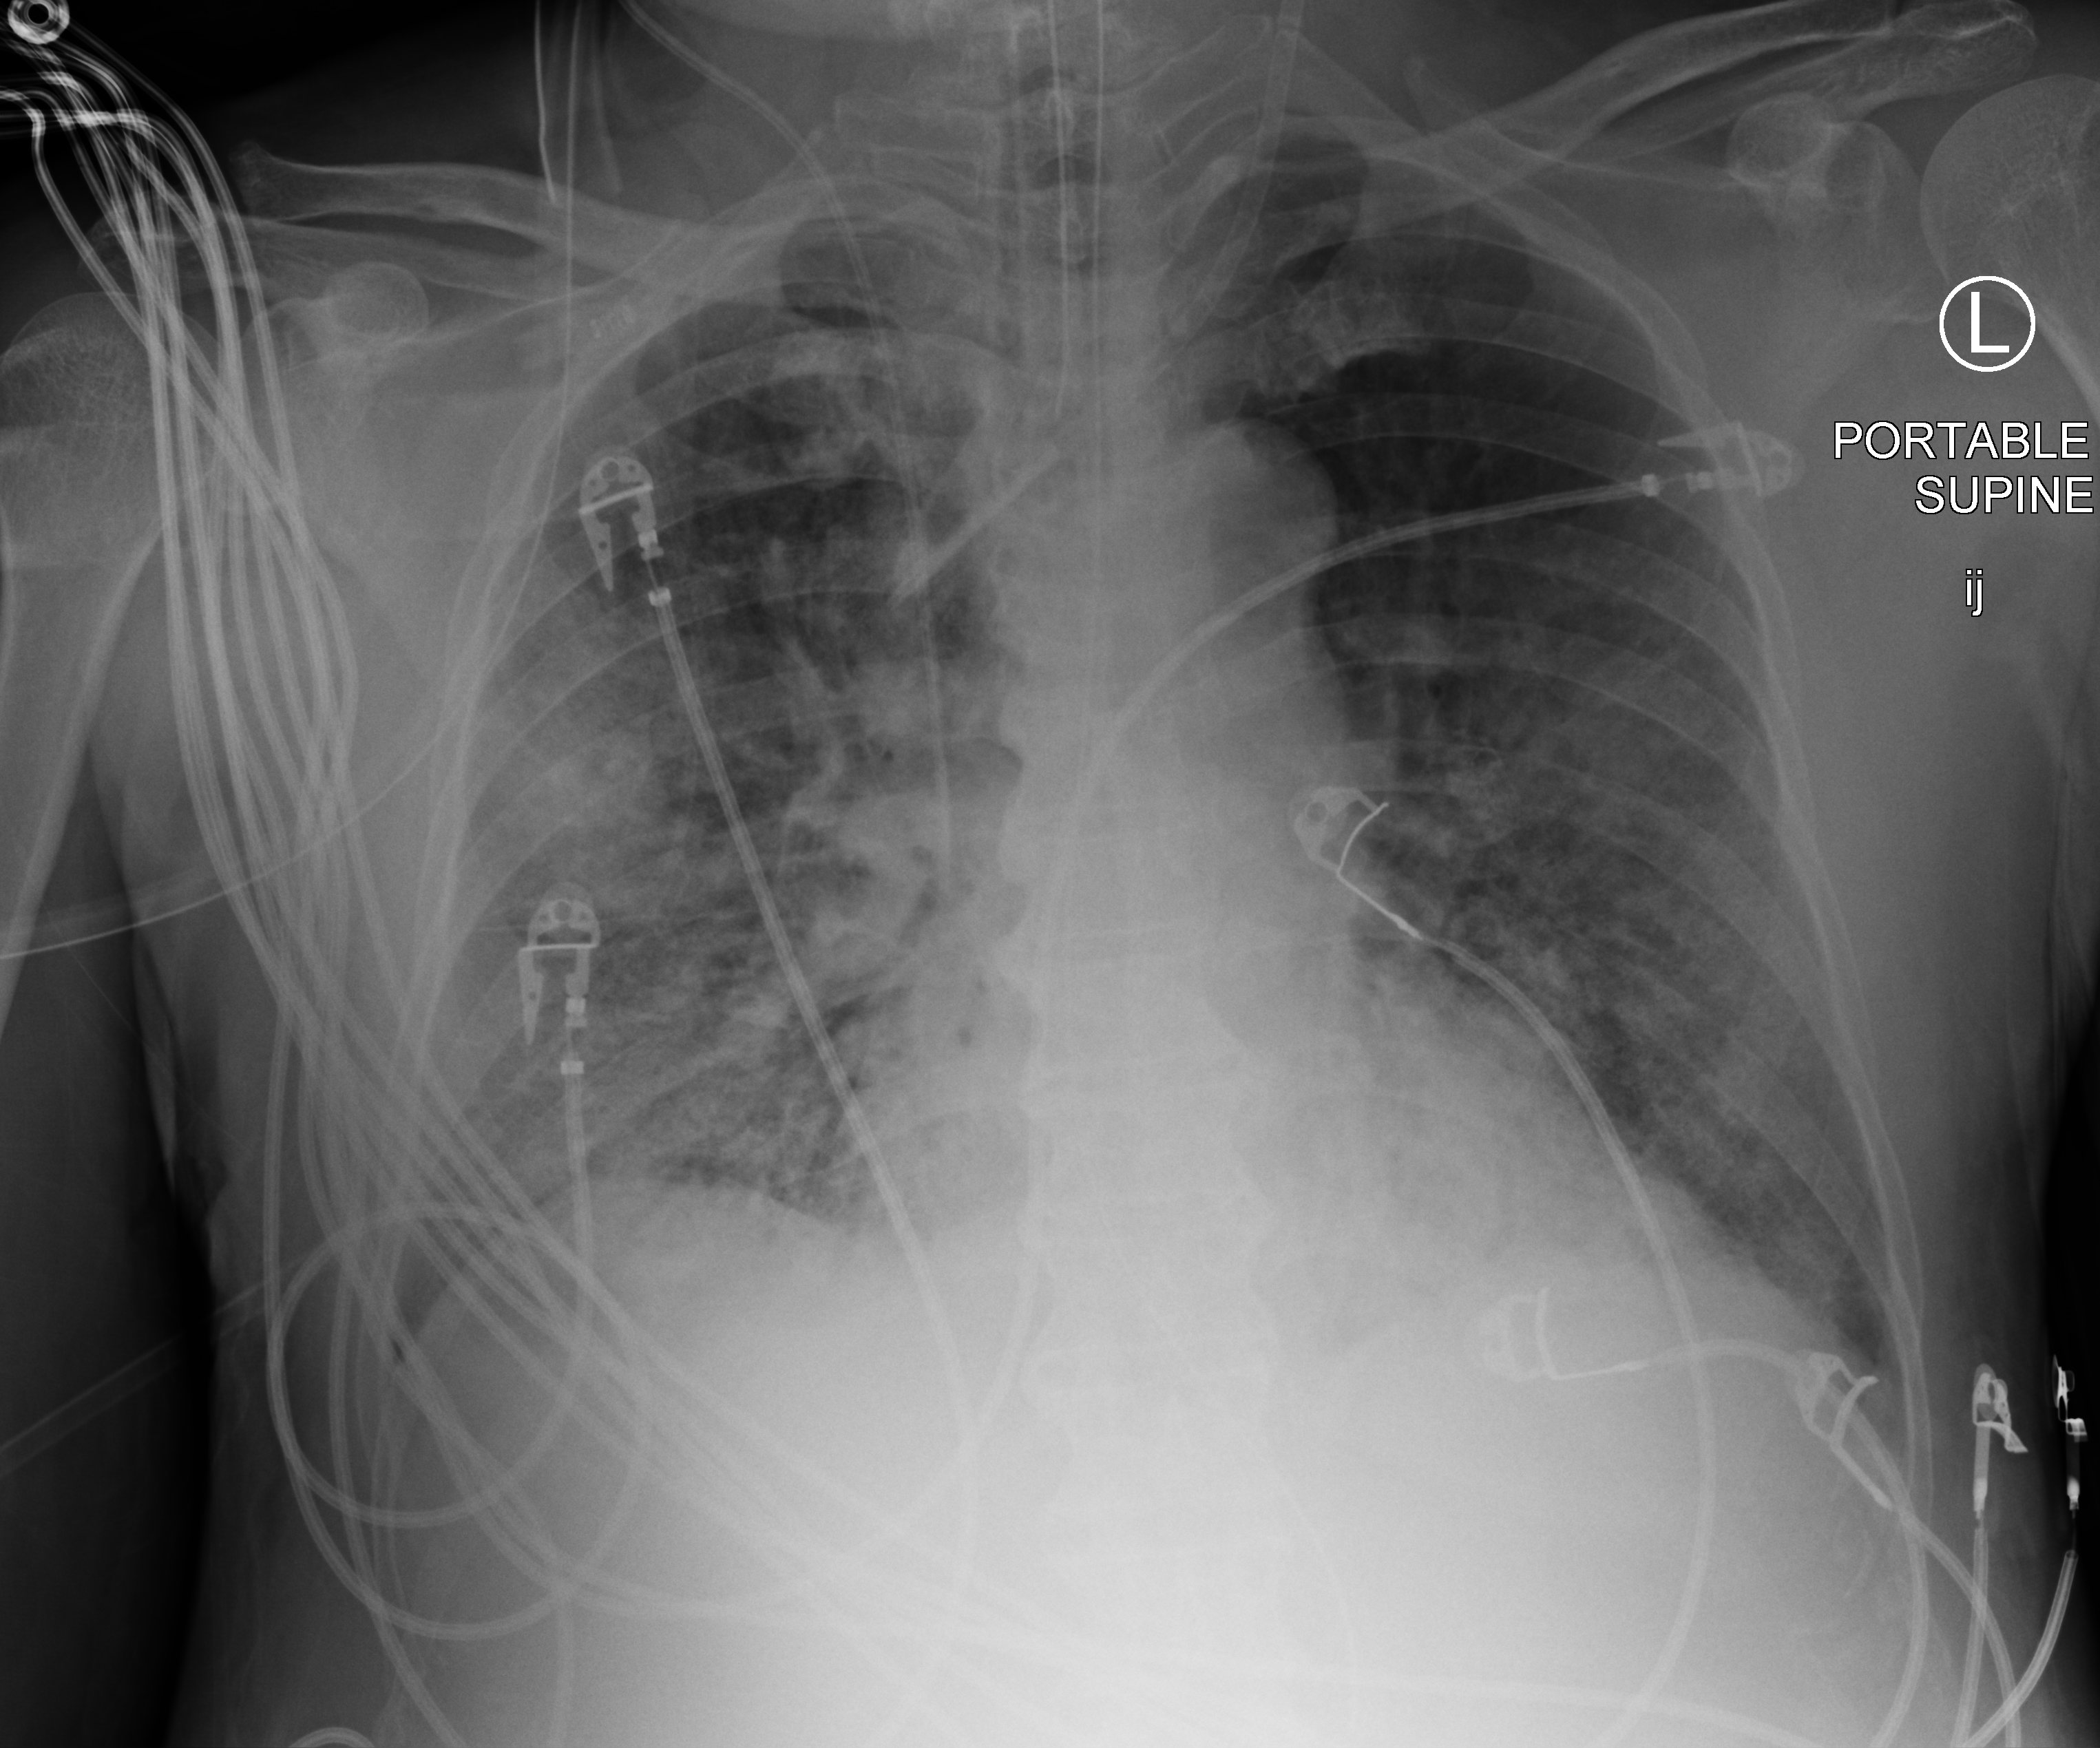
Bedside chest radiograph (computed radiography). Male patient hospitalised with COVID-19, age 60–74 years.
From the hospital-stay record, not from the radiograph (when in the stay this image was taken is not recorded): length of hospital stay: 26 days.